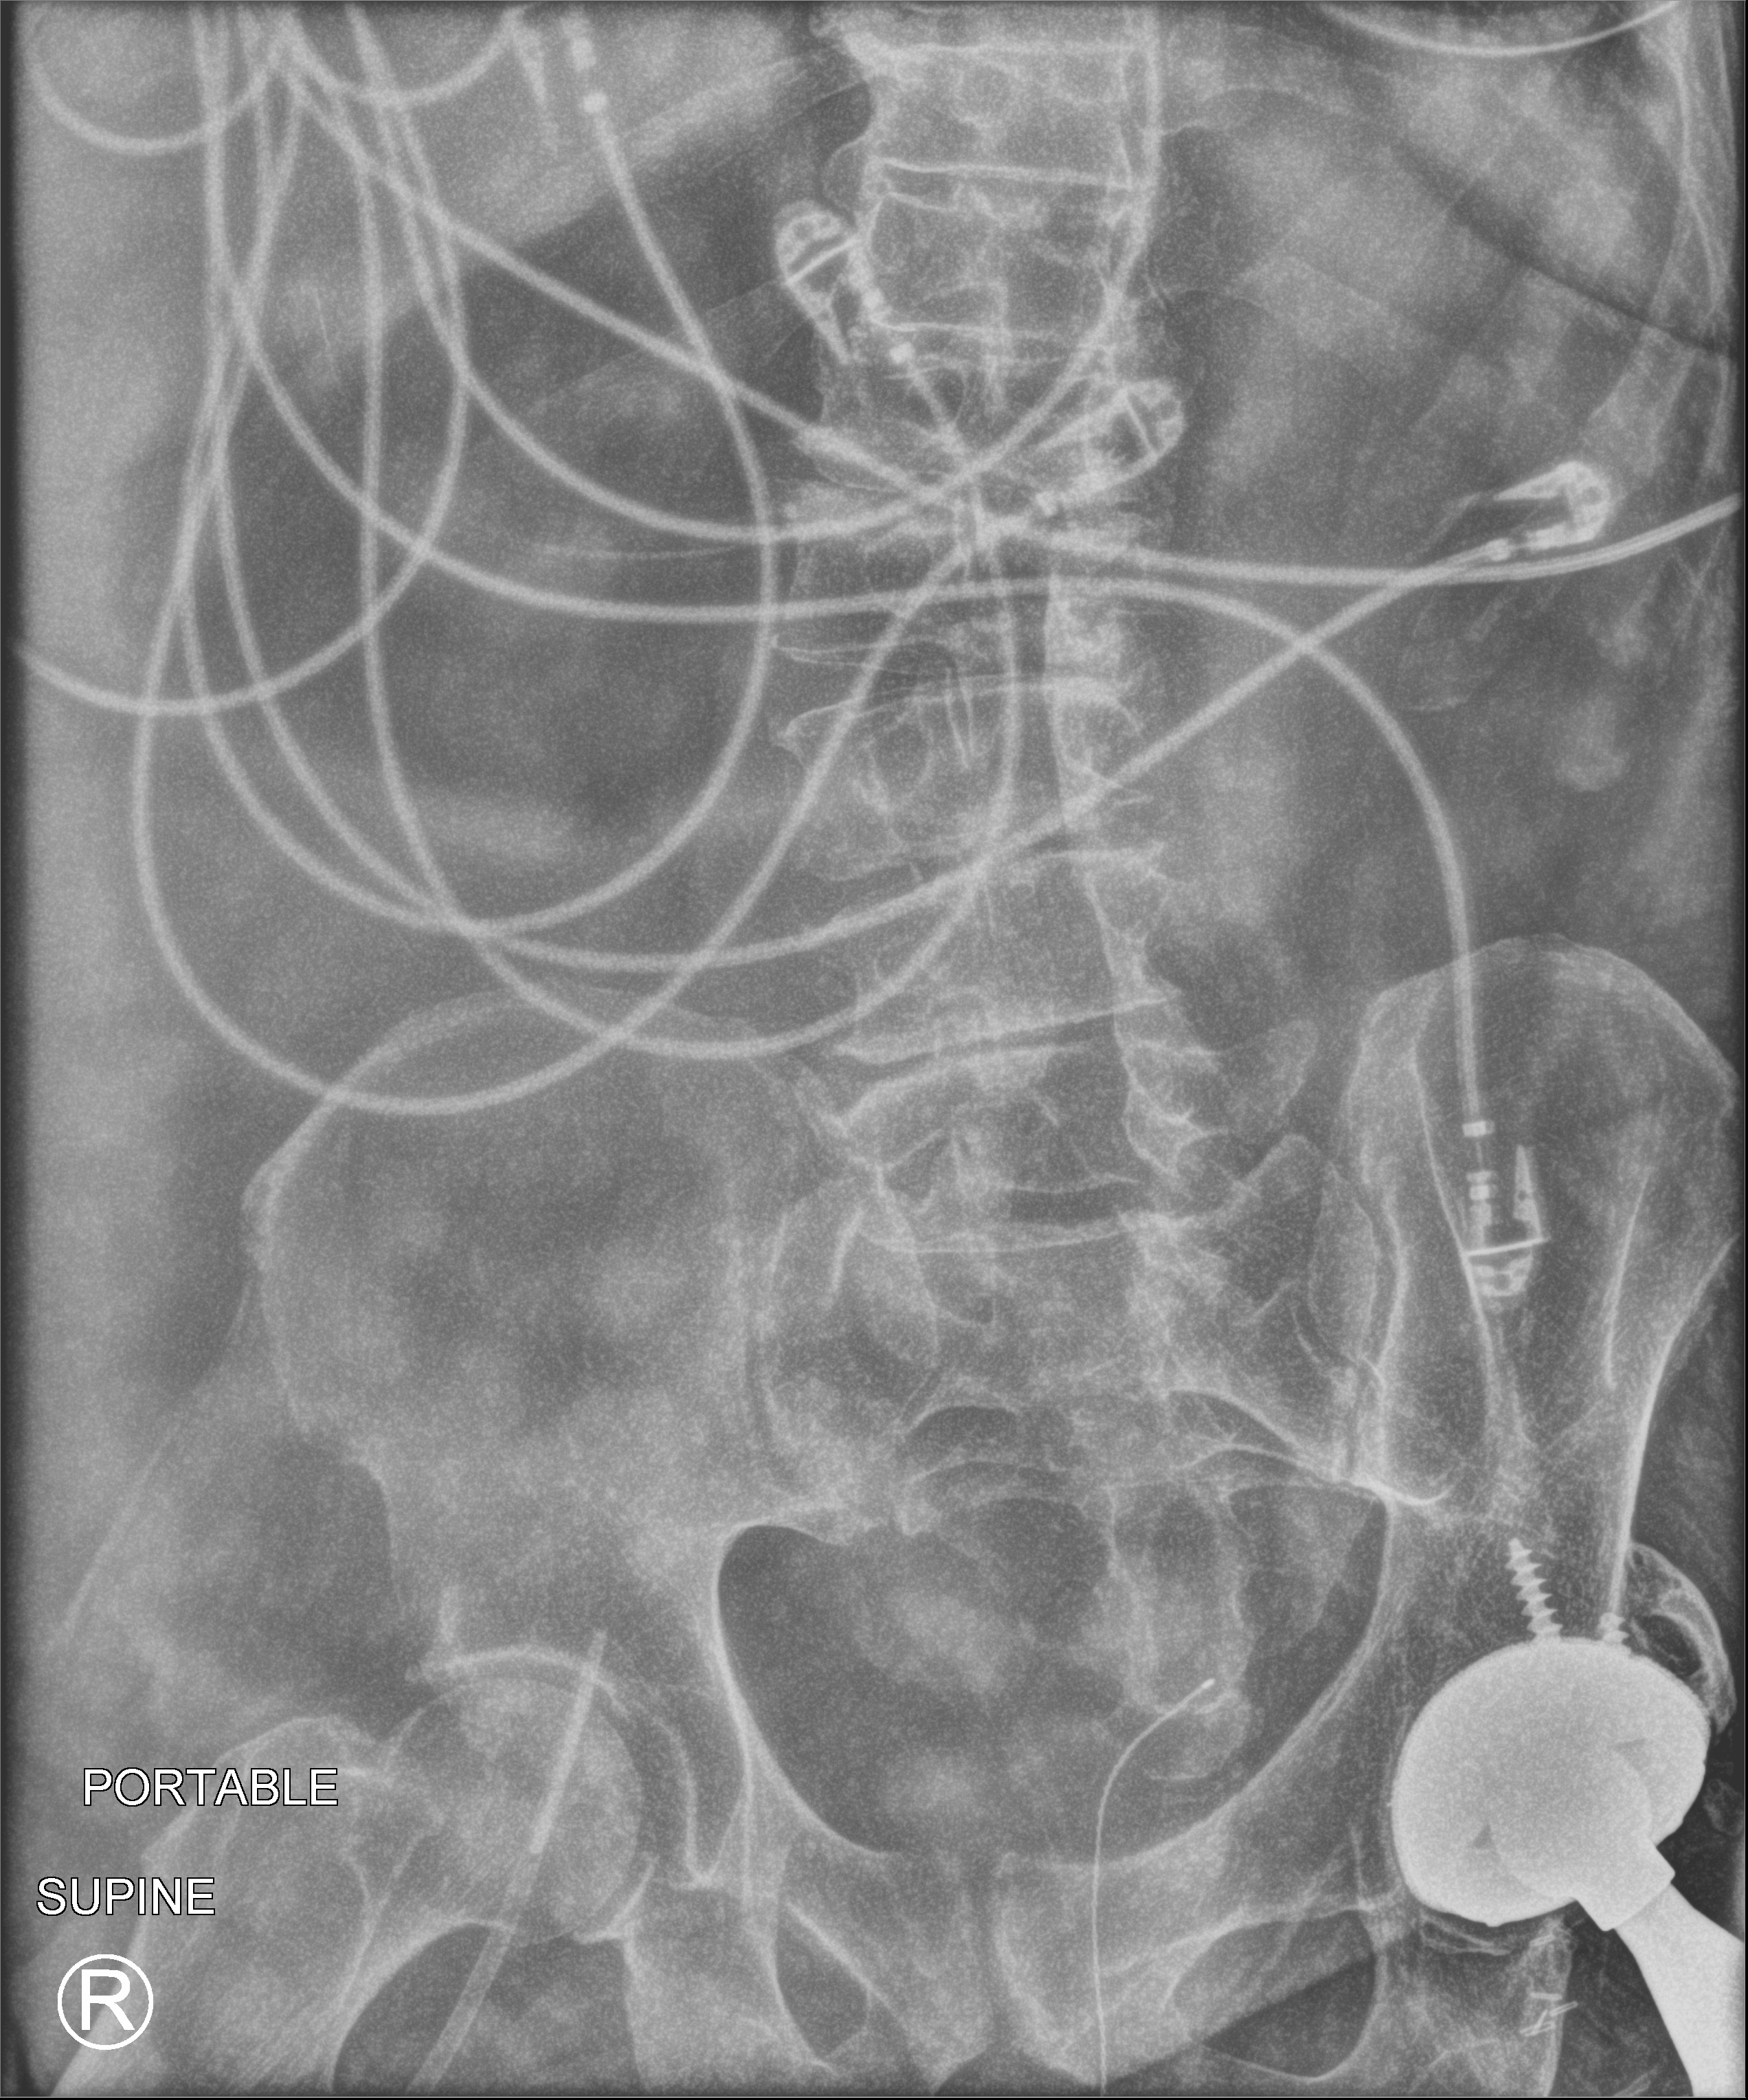
Portable abdomen radiograph, anteroposterior (AP) projection. Patient hospitalised with COVID-19; male, aged 60–74 years.
From the hospital-stay record, not from the radiograph (when in the stay this image was taken is not recorded): hypertension (admission record): no.